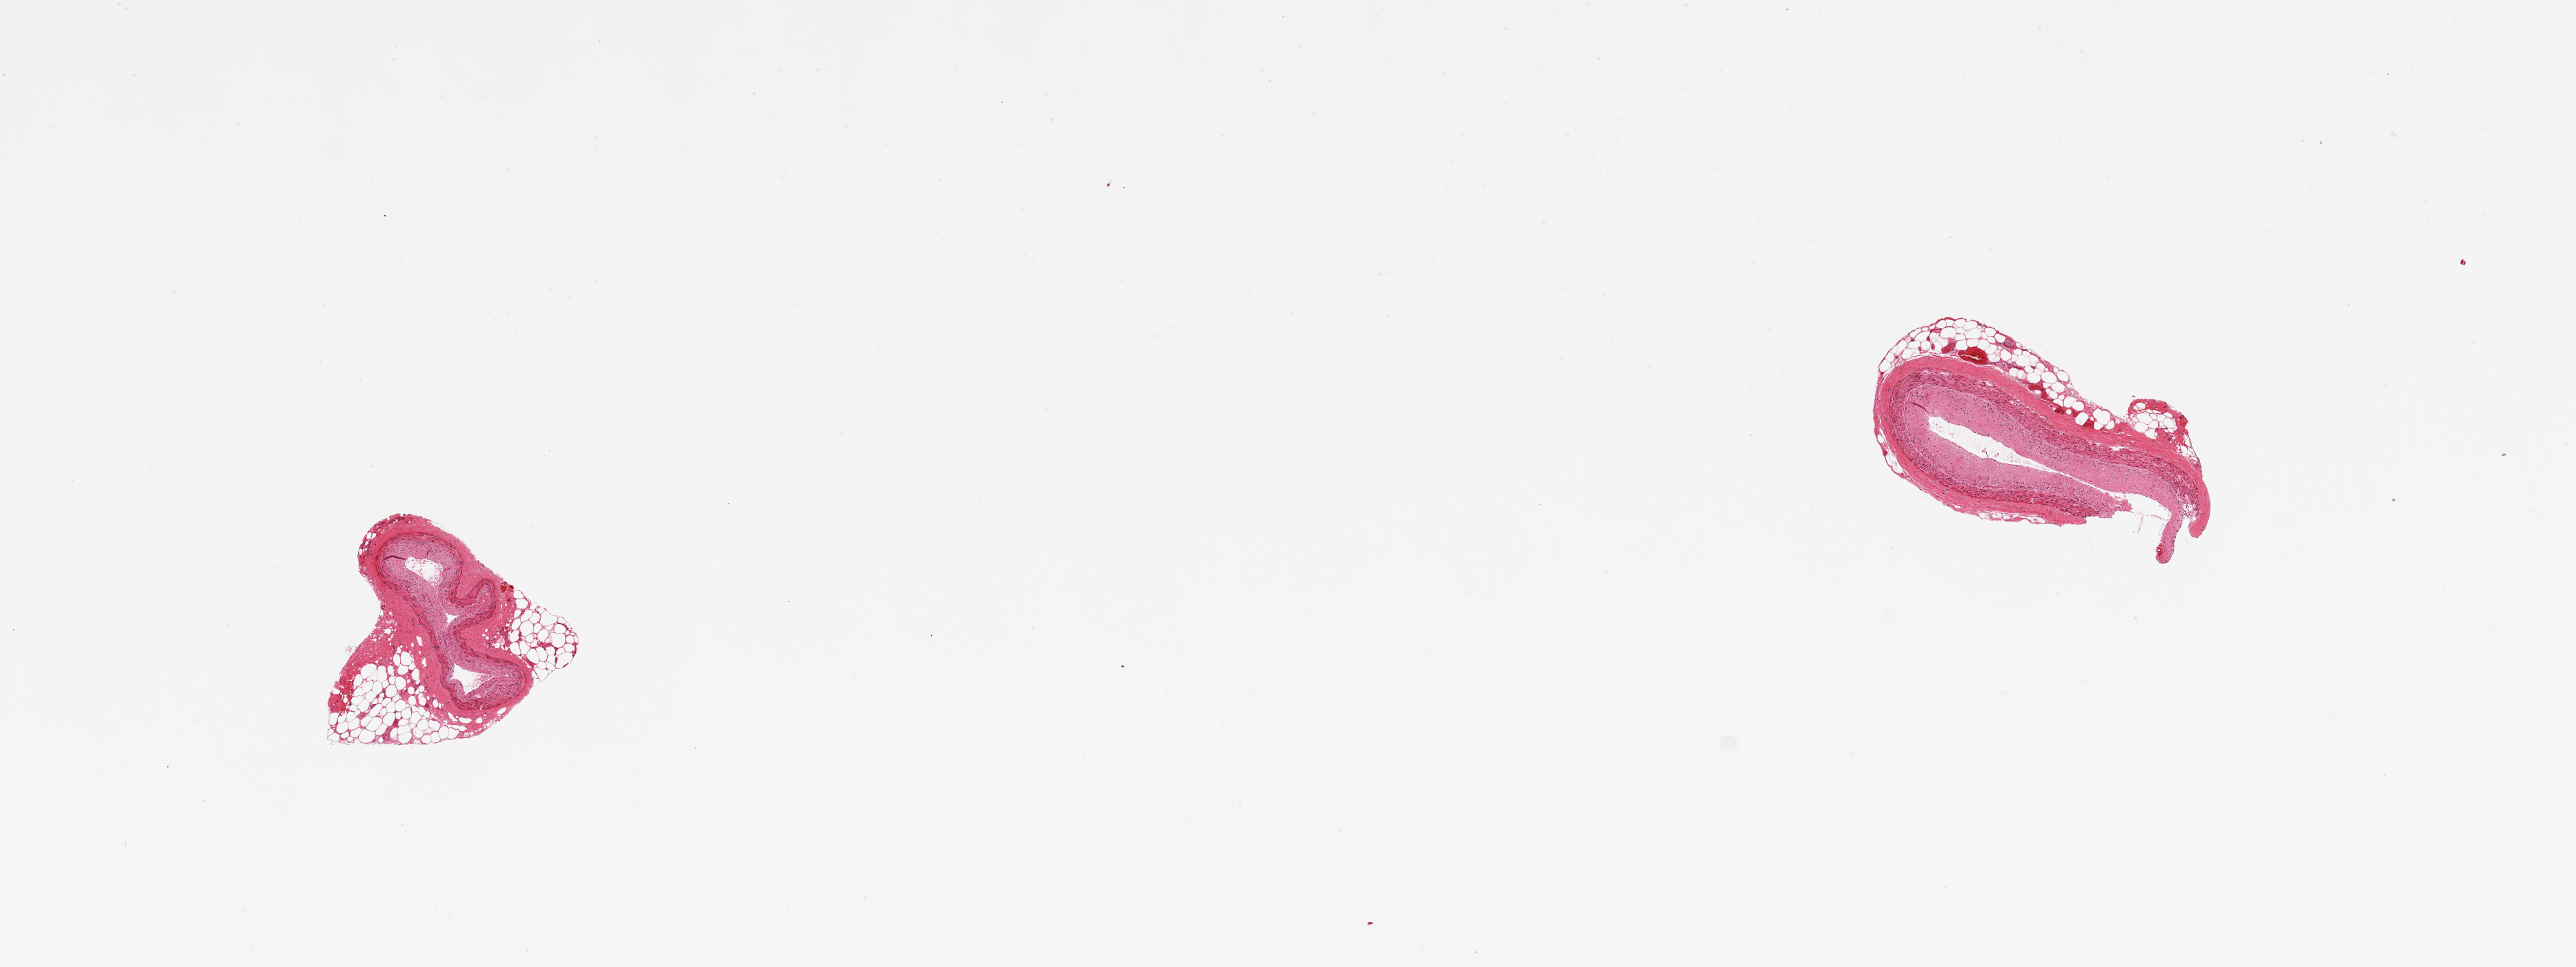
Digitized haematoxylin and eosin-stained section, brightfield, a low-resolution overview of the entire scanned area, about 14.8 x 5.5 mm (acquisition: 20x scan). PAXgene-fixed, paraffin-embedded tissue. Section of coronary artery (target tissue). Tissue donor sample. Donor sex: male.
Review note (as recorded): 2 pieces; up to 0.6mm peripheral fat; flat fibrous thickening on 1 piece.